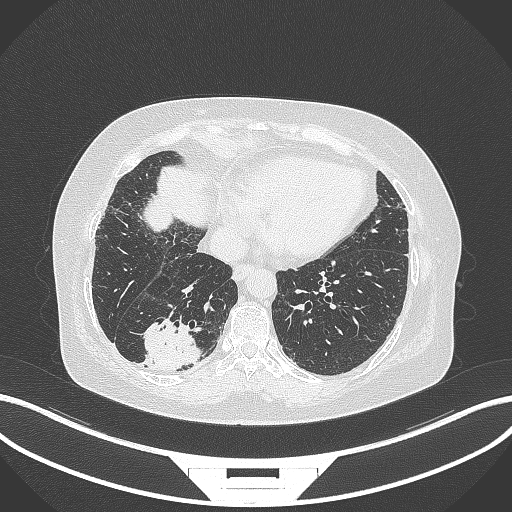
Chest CT, one axial slice; slice 65 of 296 in the series (ordered by position); 120 kVp; lung window (W 1500 / L -600 HU); 1 mm slice thickness; 512 × 512 image matrix, field of view 400 × 400 mm. Patient: female, 65 years. From the clinical record (not read from this slice): clinical TNM (as recorded): T2b N1 M0; histopathological grade: G1.
Outlined on this slice (bounding box drawn by a radiologist):
- lung tumour (recorded histology: adenocarcinoma): bounding box [x1, y1, x2, y2] px = [140, 316, 204, 372]